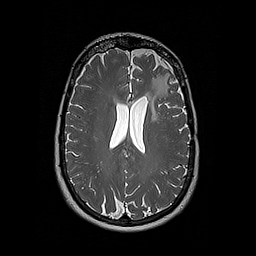
Brain MRI from a brain-tumour surgery series, one axial slice. 256 × 256 image matrix, field of view 250 × 250 mm. From the clinical record (not read from this slice): histopathology: Oligodendroglioma; WHO grade: 2; IDH mutation: yes; tumour location: Left Frontal.
Outlined on this slice (manually delineated by an expert):
- tumour: bounding box <146,76,161,120> (left, top, right, bottom; pixels)